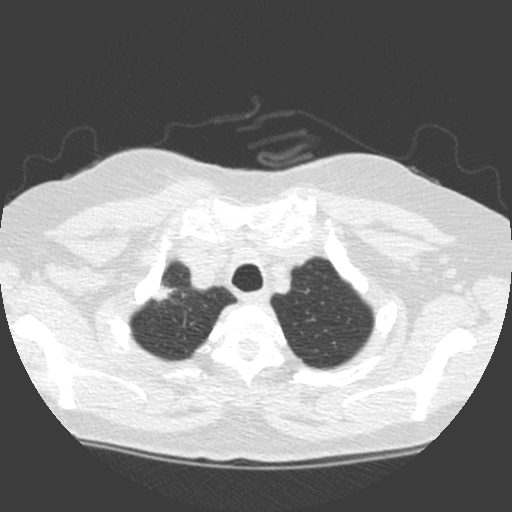
Low-dose screening chest CT, axial slice. Baseline annual screen. Lung window (W 1500 / L -600 HU). 2 mm slice thickness. Standard (soft-tissue) reconstruction kernel (C). Female, age 63 years at enrolment. Current smoker at enrolment.
Expert reader's lesion annotation, bounding box [x1, y1, x2, y2] px = [140, 276, 180, 310]. Screening reader's record for this exam (one nodule recorded; not confirmed to be the boxed lesion): non-calcified nodule or mass ≥4 mm, right upper lobe, 11 × 11 mm, spiculated (stellate) margins, soft tissue attenuation. Official screen result: positive, change unspecified: nodule(s) >= 4 mm or enlarging nodule(s), mass(es), or other non-specific abnormalities suspicious for lung cancer.